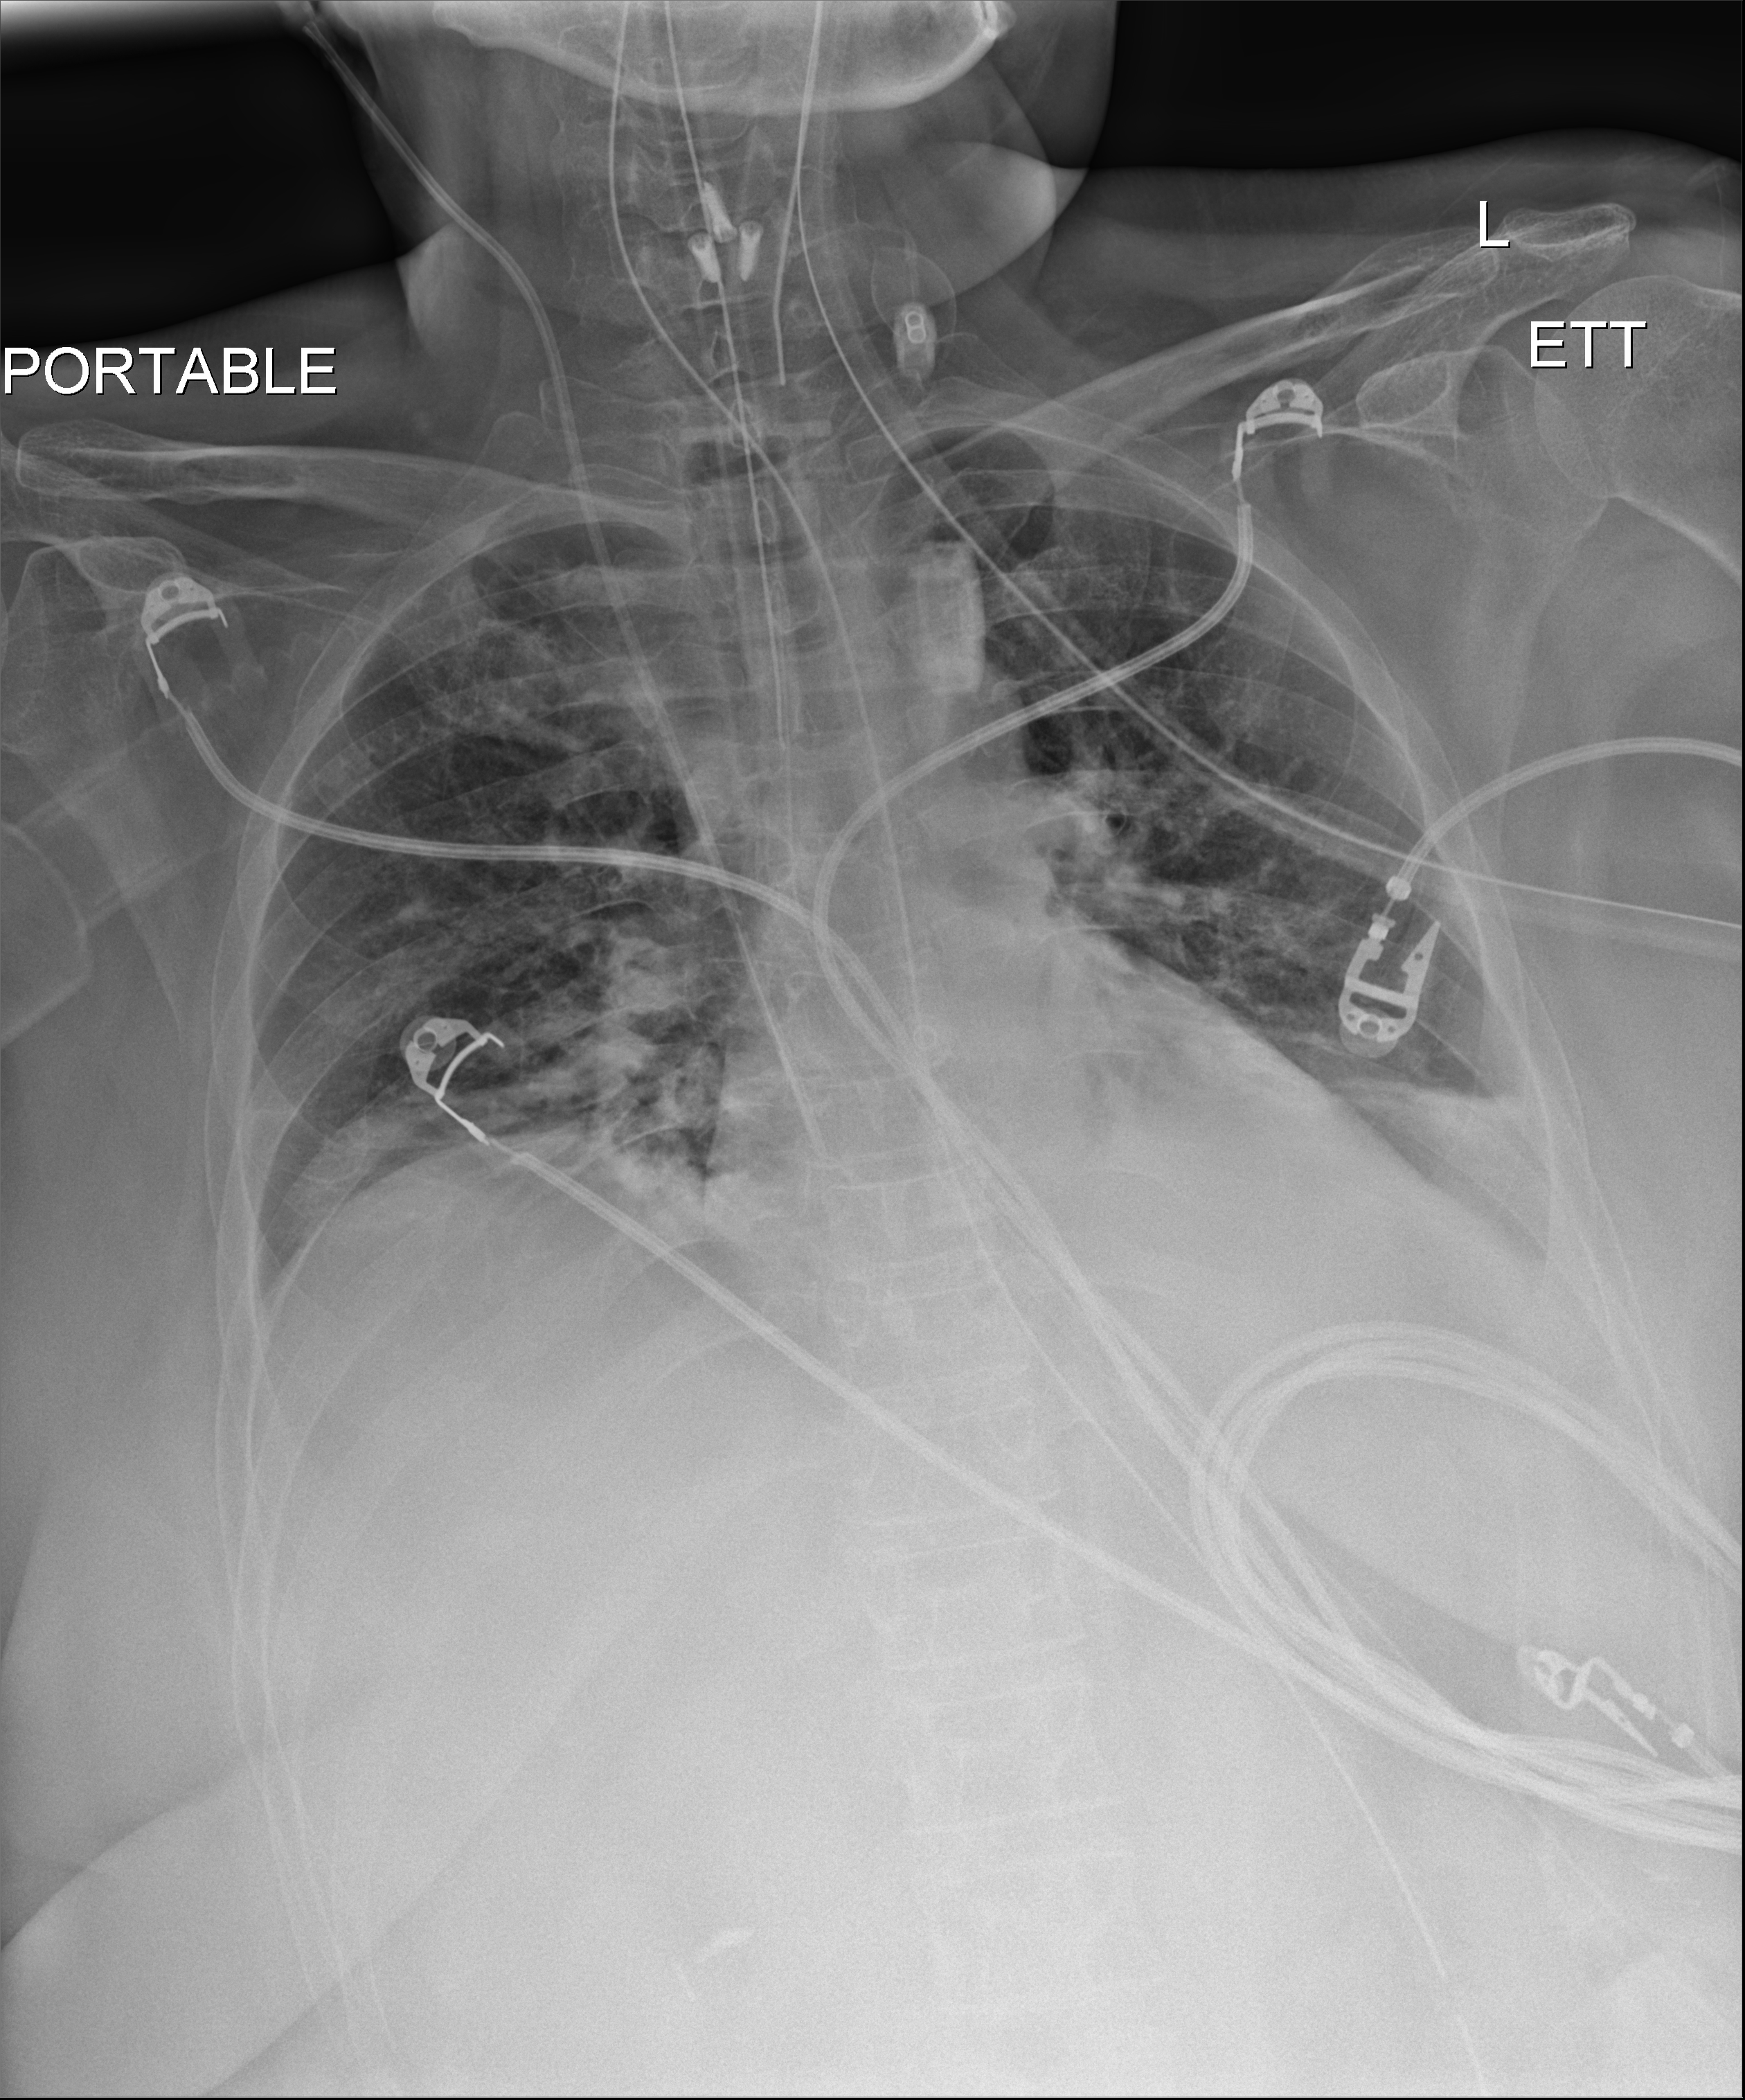
Portable chest radiograph; anteroposterior (AP) projection. Female patient hospitalised with COVID-19, age 18–59 years.
Hospital-stay facts (about this admission, not read from this image; timing relative to this image not recorded):
- mechanically ventilated during this hospital stay: no